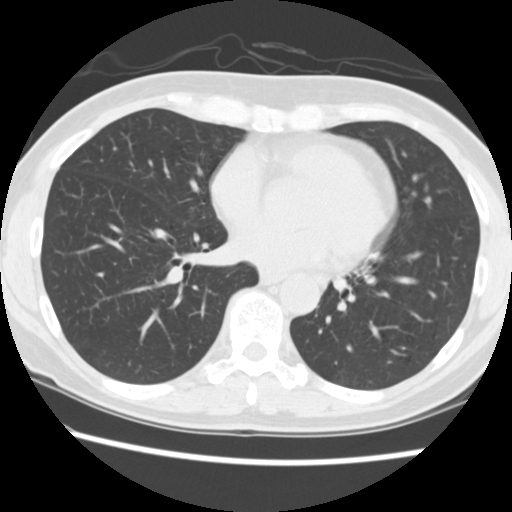
Axial slice from a low-dose chest CT screening exam, second screening round (one year after baseline), lung window (W 1500 / L -600 HU), slice 145 of 258 in the series, 512 × 512 image matrix, field of view 330 × 330 mm. Female participant, aged 60 years at enrolment. Current smoker at enrolment.
- Expert-annotated lung lesion, bounding box [x1, y1, x2, y2] px = [412, 186, 448, 222].
- Screening reader's record for this exam: no non-calcified nodule ≥4 mm recorded.
- Official screen result: negative screen, minor abnormalities not suspicious for lung cancer.
- Later outcome: lung cancer diagnosed 509 days after this screen — adenocarcinoma, NOS, lingula, poorly differentiated (G3), stage IA (AJCC 6th edition), 6 mm at pathology.